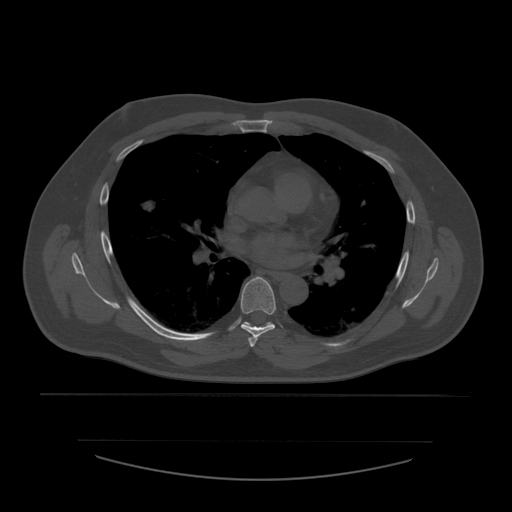
CT including the spine, one axial slice; position 376 of 532 along the scan axis; bone window (W 1800 / L 400 HU); 512 × 512 image matrix, field of view 441 × 441 mm. Patient age 44 years. From the clinical record (not read from this slice): primary cancer: soft tissue sarcoma.
Annotated regions visible in this slice (semi-automatic segmentation, software-assisted and operator-edited):
- T5 vertebra: bounding box <249,336,258,347> (left, top, right, bottom; pixels)
- T6 vertebra: <241,277,277,338>
- T7 vertebra: <245,322,270,326>